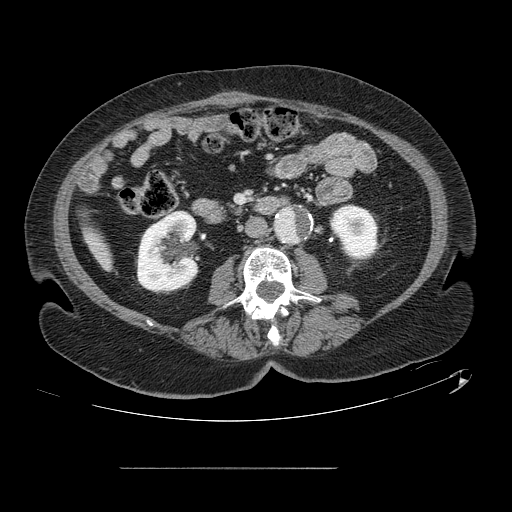
Contrast-enhanced abdominal CT, one axial slice. Slice 25 of 148 in the series (ordered by position). 120 kVp. Intravenous contrast given. Soft-tissue window (W 400 / L 40 HU). 2.5 mm slice thickness. 512 × 512 image matrix. Female patient, age 75 years. Case-level facts recorded for this patient, not image findings: diagnosis: colorectal cancer liver metastases, imaged before liver resection; multiple liver metastases: no; largest metastasis: 2.4 cm; disease in both lobes: no.
Annotated regions visible in this slice (manually delineated by an expert):
- liver: box from (x=89, y=231) to (x=112, y=268) px
- planned liver remnant (the part of the liver to remain after resection): (x=90, y=233)–(x=111, y=266)